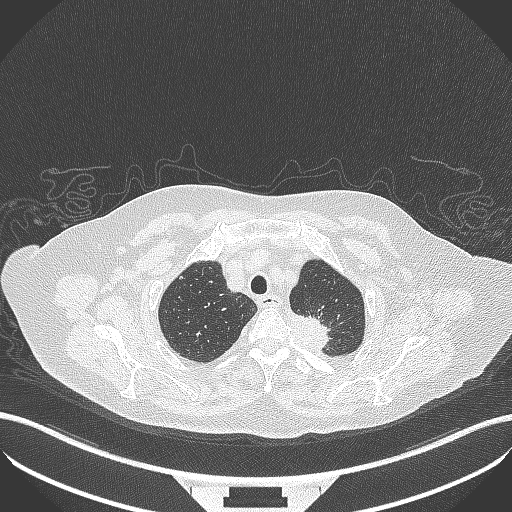
Chest CT, one axial slice; position 294 of 353 along the scan axis; lung window (W 1500 / L -600 HU); 1 mm slice thickness; 512 × 512 image matrix, field of view 400 × 400 mm. Patient: female, 81 years. From the clinical record (not read from this slice): clinical TNM (as recorded): T2a N0 M0.
Structures marked on this image (bounding box drawn by a radiologist):
- lung tumour (recorded histology: adenocarcinoma): bounding box <284,306,342,354> (left, top, right, bottom; pixels)